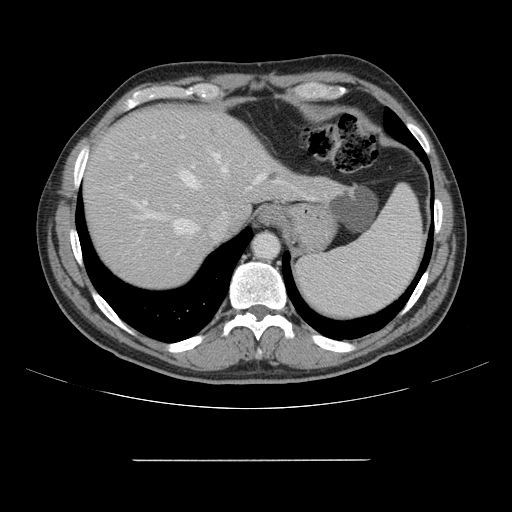
Contrast-enhanced abdominal CT, one axial slice. Slice 125 of 164 in the series (ordered by position). Soft-tissue window (W 400 / L 40 HU). 2.5 mm slice thickness. 512 × 512 image matrix, field of view 404 × 404 mm. Male patient, age 54 years. From the clinical record (not read from this slice): diagnosis: colorectal cancer liver metastases, imaged before liver resection; multiple liver metastases: yes; largest metastasis: 1 cm.
Structures marked on this image (outlined manually by an expert reader):
- hepatic veins: bounding box (x1, y1, x2, y2) in pixels: (140, 154, 315, 234)
- liver: (85, 107, 337, 287)
- planned liver remnant (the part of the liver to remain after resection): (84, 107, 255, 286)
- portal vein (with intrahepatic branches): (110, 135, 216, 271)
- liver metastasis: (270, 173, 278, 182)